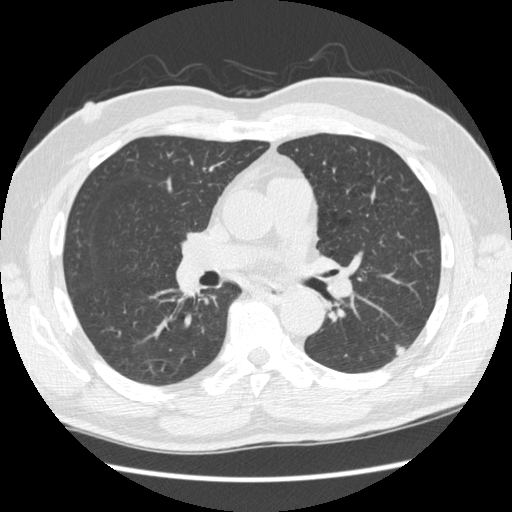
Low-dose screening chest CT, axial slice, baseline screening round, lung window (W 1500 / L -600 HU), 1.25 mm slice thickness, slice 117 of 267 in the series. Male, age 74 years at enrolment. Former smoker at enrolment.
- Lesion marked by an expert reader, box from (x=370, y=324) to (x=414, y=366) px.
- The screening reader recorded 3 non-calcified nodules or masses ≥4 mm on this exam (right upper lobe, right lower lobe, left upper lobe); which of them this box marks is not recorded.
- Later outcome: lung cancer diagnosed 384 days after this screen (after the second annual screen) — squamous cell carcinoma, NOS, left lower lobe, well differentiated (G1), stage IA (AJCC 6th edition), 28 mm at pathology.